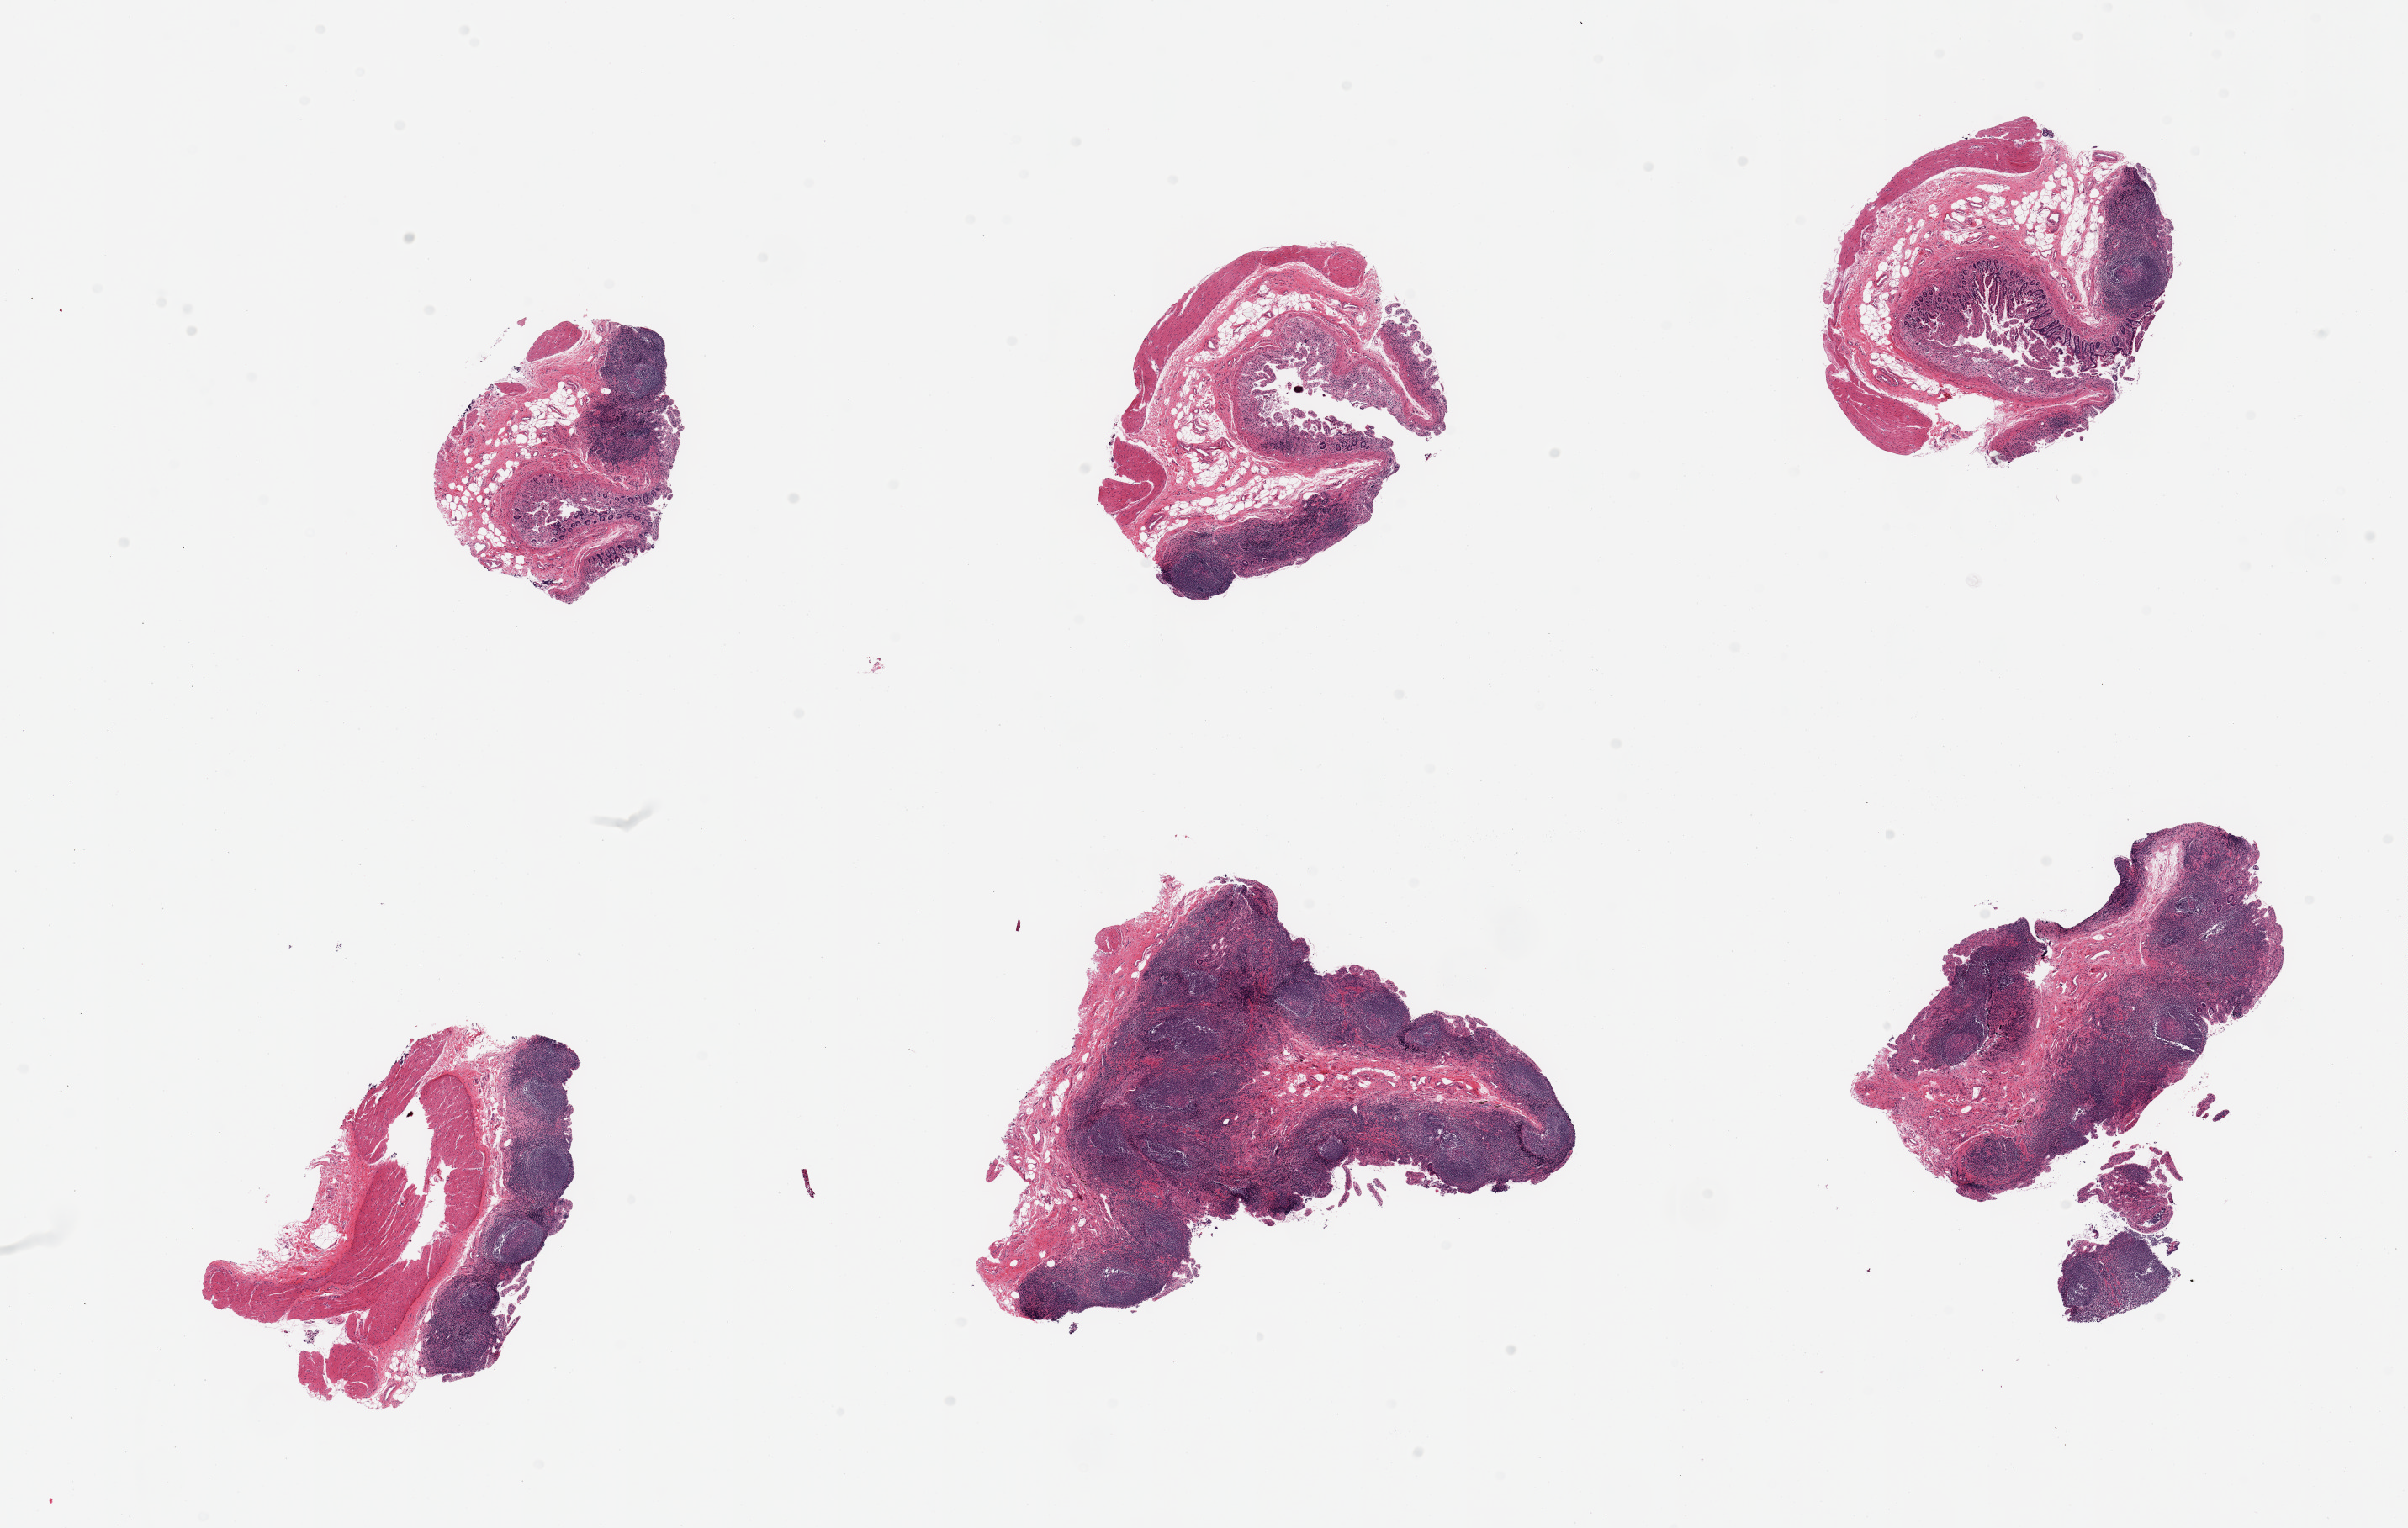
Digitized H&E-stained section — whole scanned area (about 22.6 x 14.4 mm) shown as a low-resolution overview; PAXgene-fixed paraffin-embedded (PFPE) section; sampled site (target tissue): ileum; donor tissue sample. Male donor.
* pathologist's review note for this sample: 6 pieces, well preserved, abundant lymphoid aggregates are 50-60% of tissue